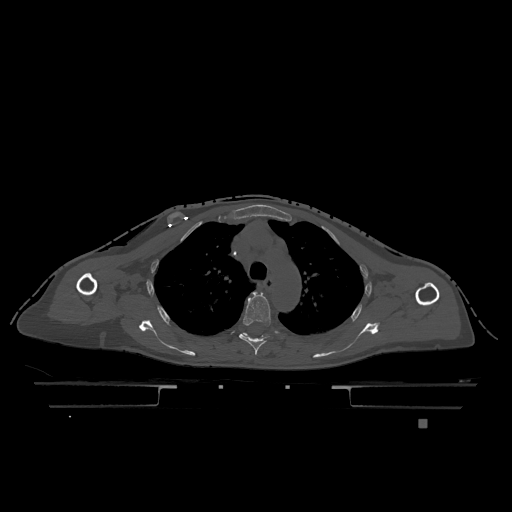
CT including the spine, one axial slice; position 876 of 1317 along the scan axis; bone window (W 1800 / L 400 HU); 512 × 512 image matrix, field of view 500 × 500 mm. Patient: female, 74 years. From the clinical record (not read from this slice): primary cancer: lung; vertebrae with lytic lesions (as recorded): T1, T4, T5, T6, L4, L5.
Structures marked on this image (semi-automatically segmented with operator editing):
- T4 vertebra: bounding box <239,292,273,355> (left, top, right, bottom; pixels)
- T5 vertebra: <243,333,247,336>